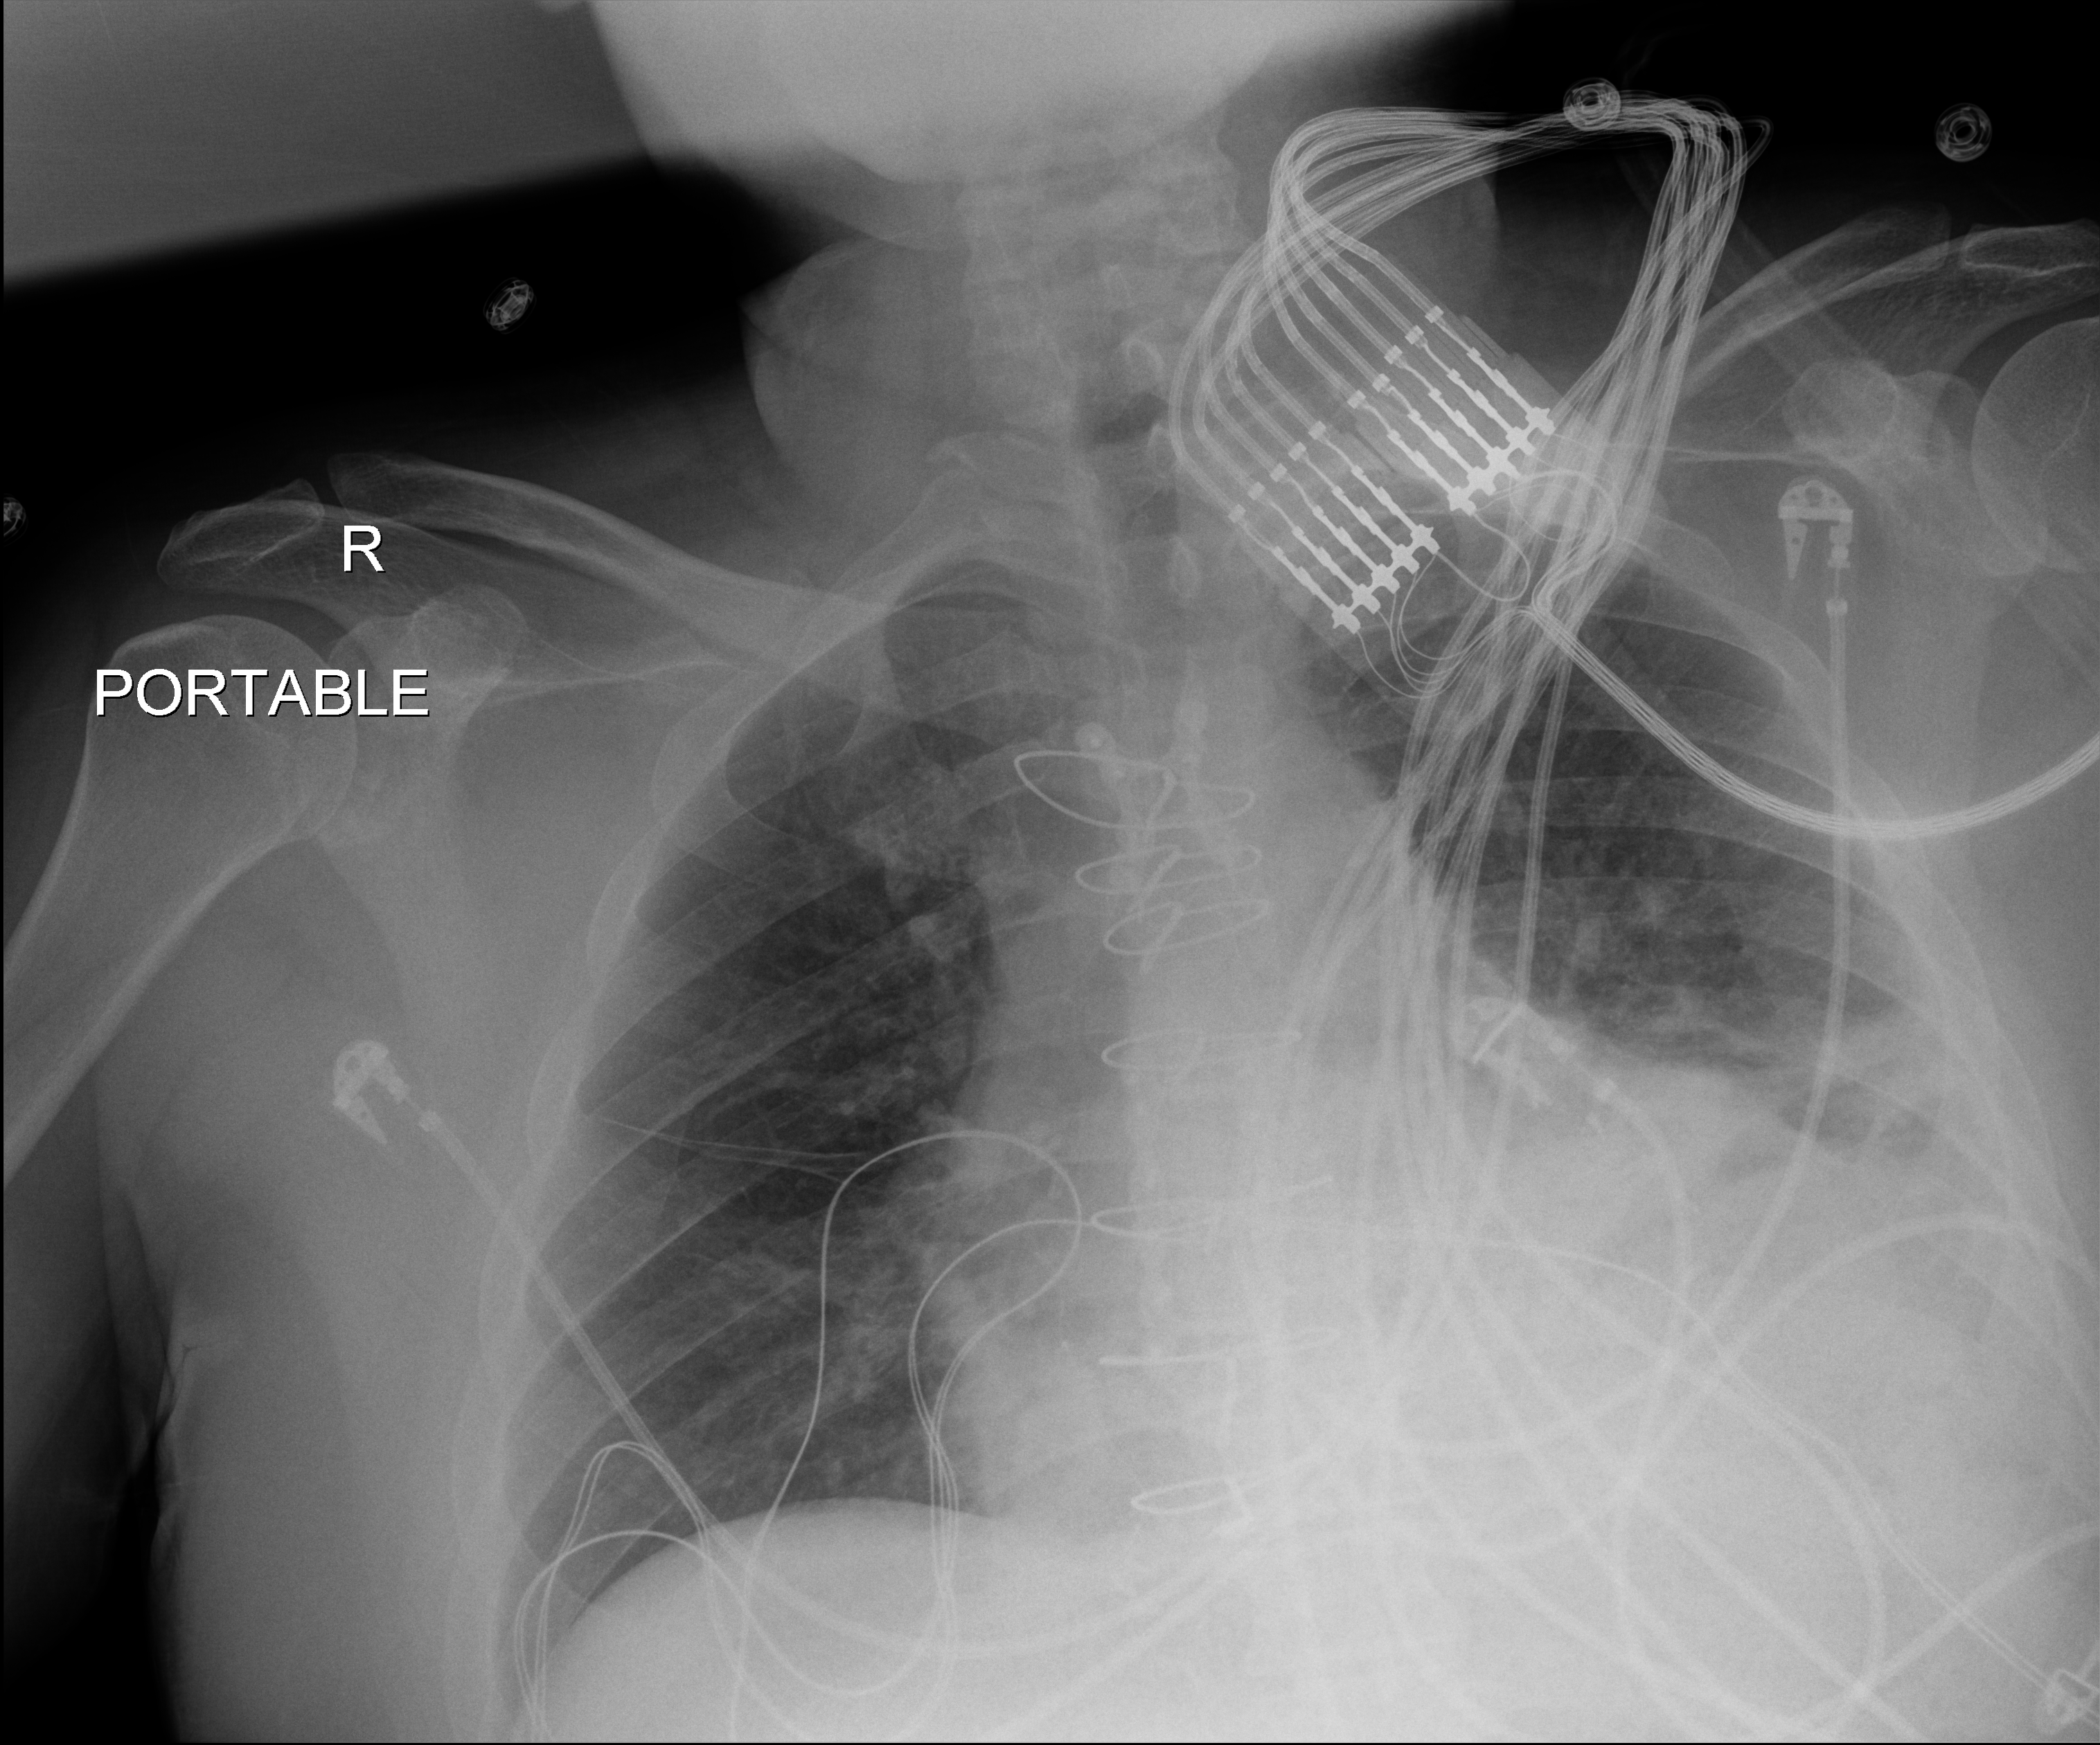
Chest radiograph; anteroposterior (AP) projection. Male patient hospitalised with COVID-19, age 18–59 years.
Hospital-stay facts (about this admission, not read from this image; timing relative to this image not recorded): mechanically ventilated during this hospital stay: no.